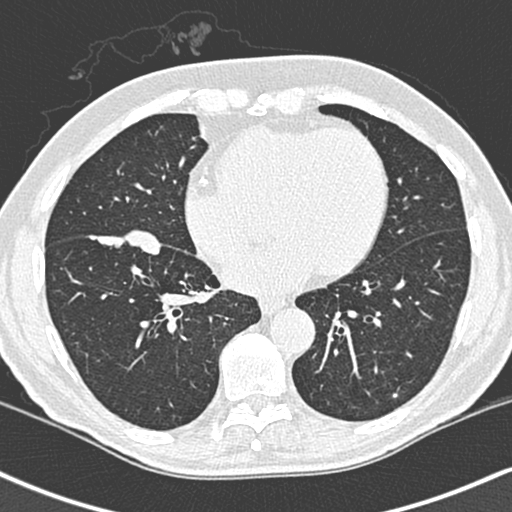
Low-dose screening chest CT, one axial slice. Position 107 of 248 along the scan axis. 120 kVp. Lung window (W 1500 / L -600 HU). 1.3 mm slice thickness. 512 × 512 image matrix.
Annotated regions visible in this slice (outlined manually by an expert reader):
- lesion 1 (tumor, lower lobe of right lung): bounding box [x1, y1, x2, y2] px = [89, 192, 162, 217]